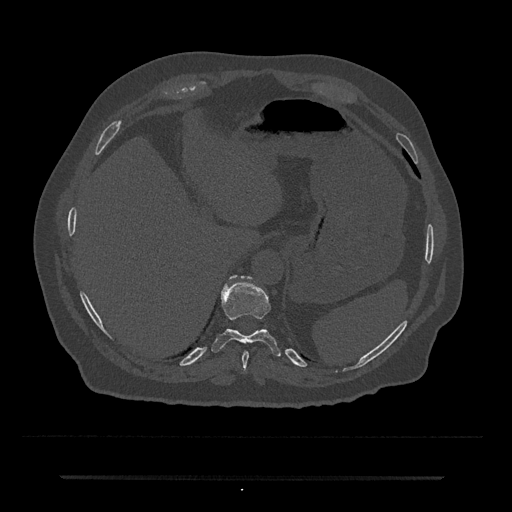
CT including the spine, one axial slice. Reconstruction kernel Br40s/3. 120 kVp. Bone window (W 1800 / L 400 HU). 512 × 512 image matrix. Patient: male, 69 years. From the clinical record (not read from this slice): primary cancer: prostate.
Structures marked on this image (semi-automatically segmented with operator editing):
- T10 vertebra: bounding box (x1, y1, x2, y2) in pixels: (211, 275, 281, 357)
- T11 vertebra: (230, 275, 243, 281)
- T9 vertebra: (242, 350, 249, 370)